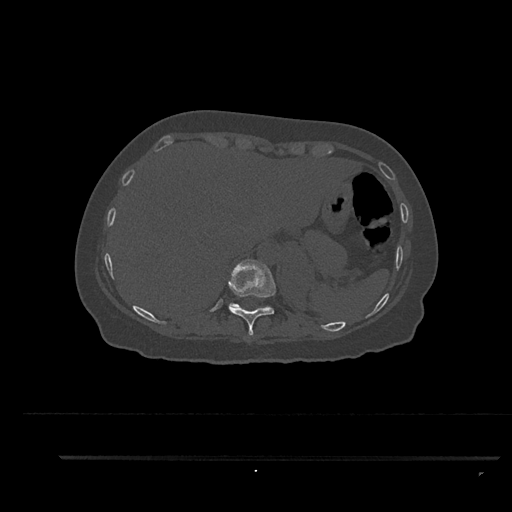
CT including the spine, one axial slice; reconstruction kernel Br40s/3; 120 kVp; bone window (W 1800 / L 400 HU); 0.5 mm slice thickness; 512 × 512 image matrix, field of view 408 × 408 mm. Female patient, age 44 years. From the clinical record (not read from this slice): primary cancer: renal; vertebrae with lytic lesions (as recorded): L1.
Annotated regions visible in this slice (semi-automatic segmentation, software-assisted and operator-edited):
- T10 vertebra: box from (x=228, y=259) to (x=276, y=336) px
- T11 vertebra: (x=229, y=302)–(x=239, y=306)